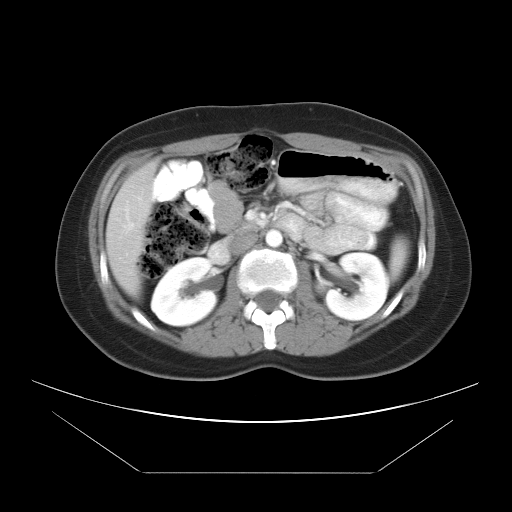
Contrast-enhanced abdominal CT, one axial slice. Slice 18 of 34 in the series (ordered by position). 120 kVp. Soft-tissue window (W 400 / L 40 HU). 7.5 mm slice thickness. 512 × 512 image matrix, field of view 410 × 410 mm. Female patient, age 38 years. From the clinical record (not read from this slice): diagnosis: colorectal cancer liver metastases, imaged before liver resection; multiple liver metastases: yes; largest metastasis: 3.1 cm; disease in both lobes: no.
Outlined on this slice (manually delineated by an expert):
- liver: box from (x=107, y=160) to (x=160, y=299) px